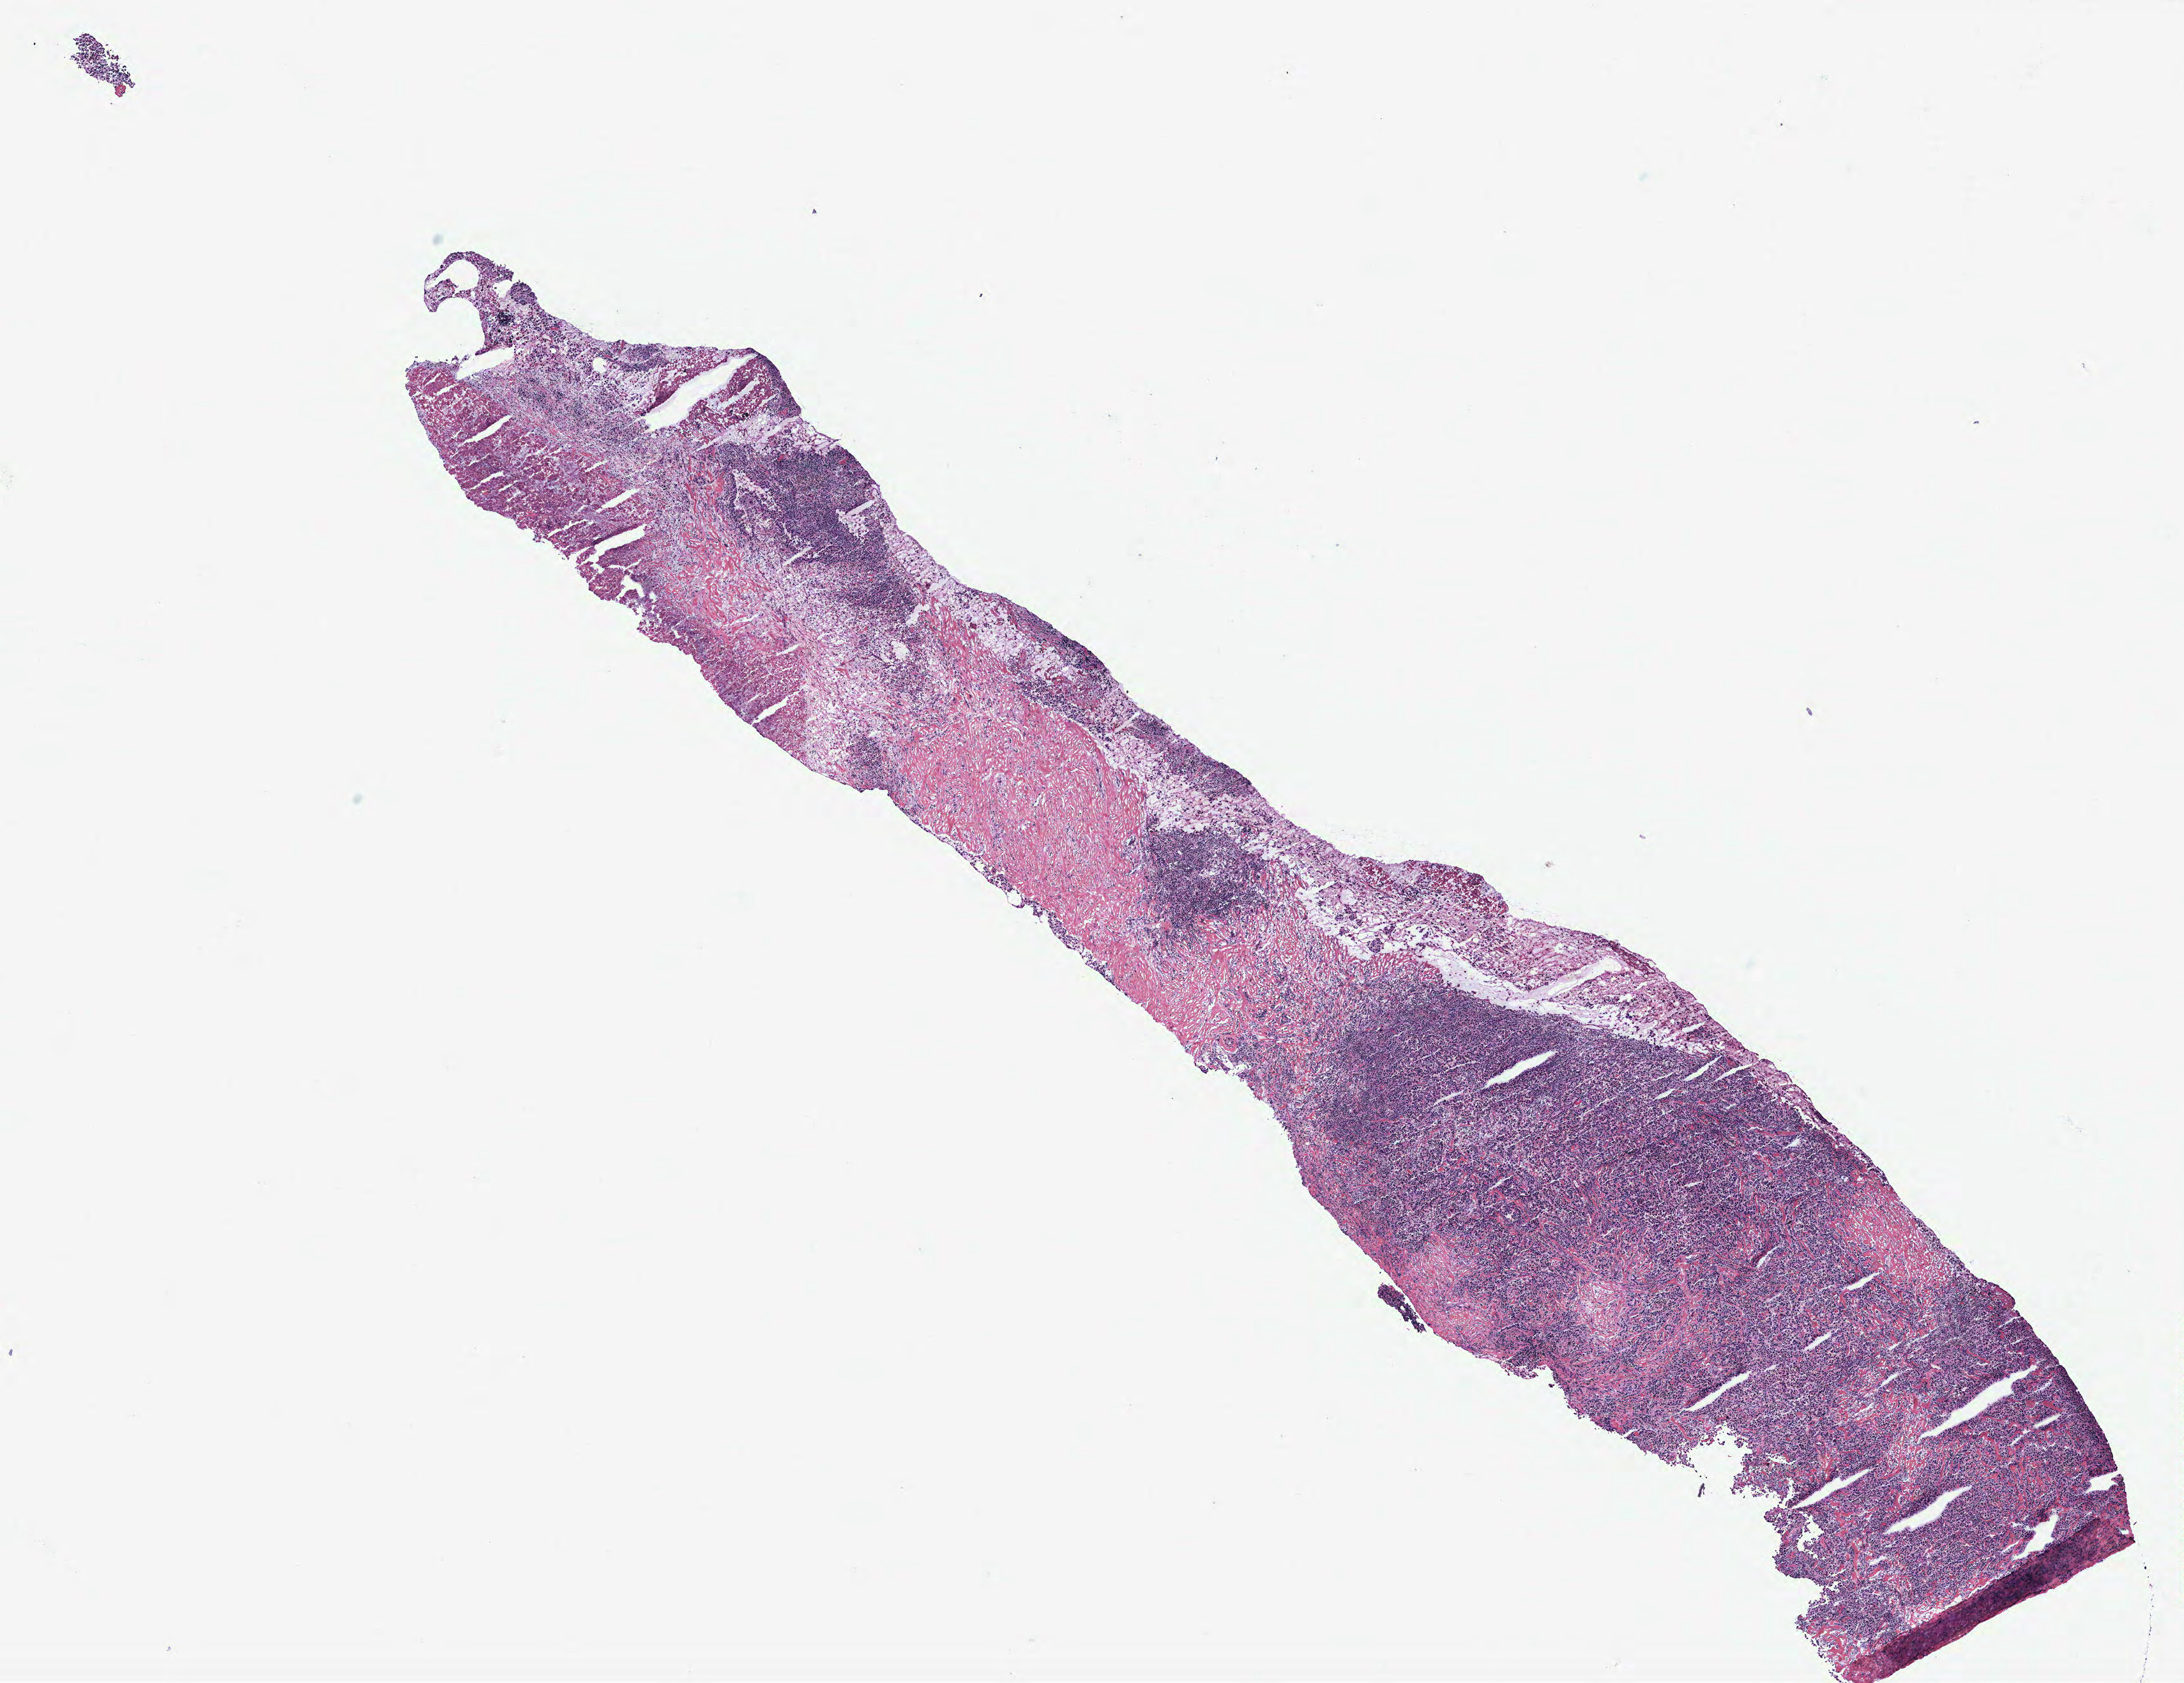
H&E-stained whole-slide image, low-resolution overview of the scanned area, about 13.7 x 10.5 mm (slide scanned at 40x), breast, tumour tissue. 84-year-old female patient.
AJCC pathologic stage: IIIA. Diagnosis: Infiltrating duct carcinoma, NOS.